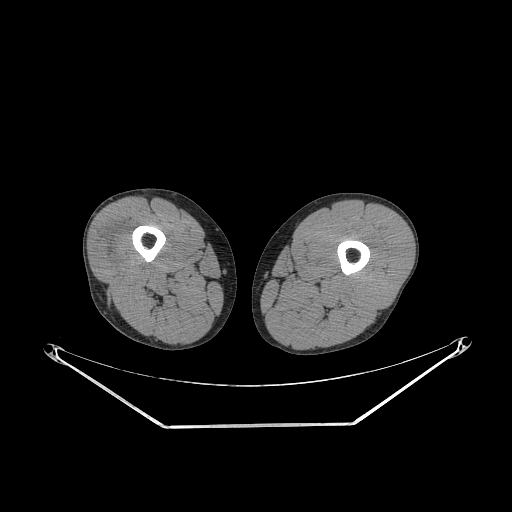
CT of an extremity soft-tissue mass (from a PET/CT study), one axial slice; position 220 of 267 along the scan axis; reconstruction kernel STANDARD; 140 kVp; soft-tissue window (W 400 / L 40 HU); 3.75 mm slice thickness; 512 × 512 image matrix, field of view 500 × 500 mm. Male patient. From the clinical record (not read from this slice): histological type: poorly differentiated synovial sarcoma; grade: high; site of the primary tumour: right buttock.
Structures marked on this image (expert contour drawn on MRI and transferred to this co-registered scan by the dataset authors):
- gross tumour volume including surrounding oedema: bounding box <101,235,133,270> (left, top, right, bottom; pixels)